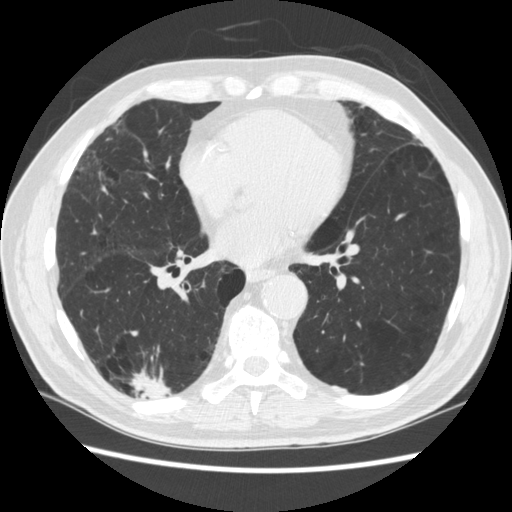
Axial slice from a low-dose chest CT screening exam, third annual screen, lung window (W 1500 / L -600 HU), 120 kVp, slice 150 of 266 in the series. Male, age 70 years at enrolment. Former smoker at enrolment.
Expert reader's lesion annotation, box from (x=124, y=360) to (x=181, y=418) px. The screening reader recorded 4 non-calcified nodules or masses ≥4 mm on this exam (right lower lobe, right lower lobe, left lower lobe, left lower lobe); which of them this box marks is not recorded. Official screen result: positive, other.